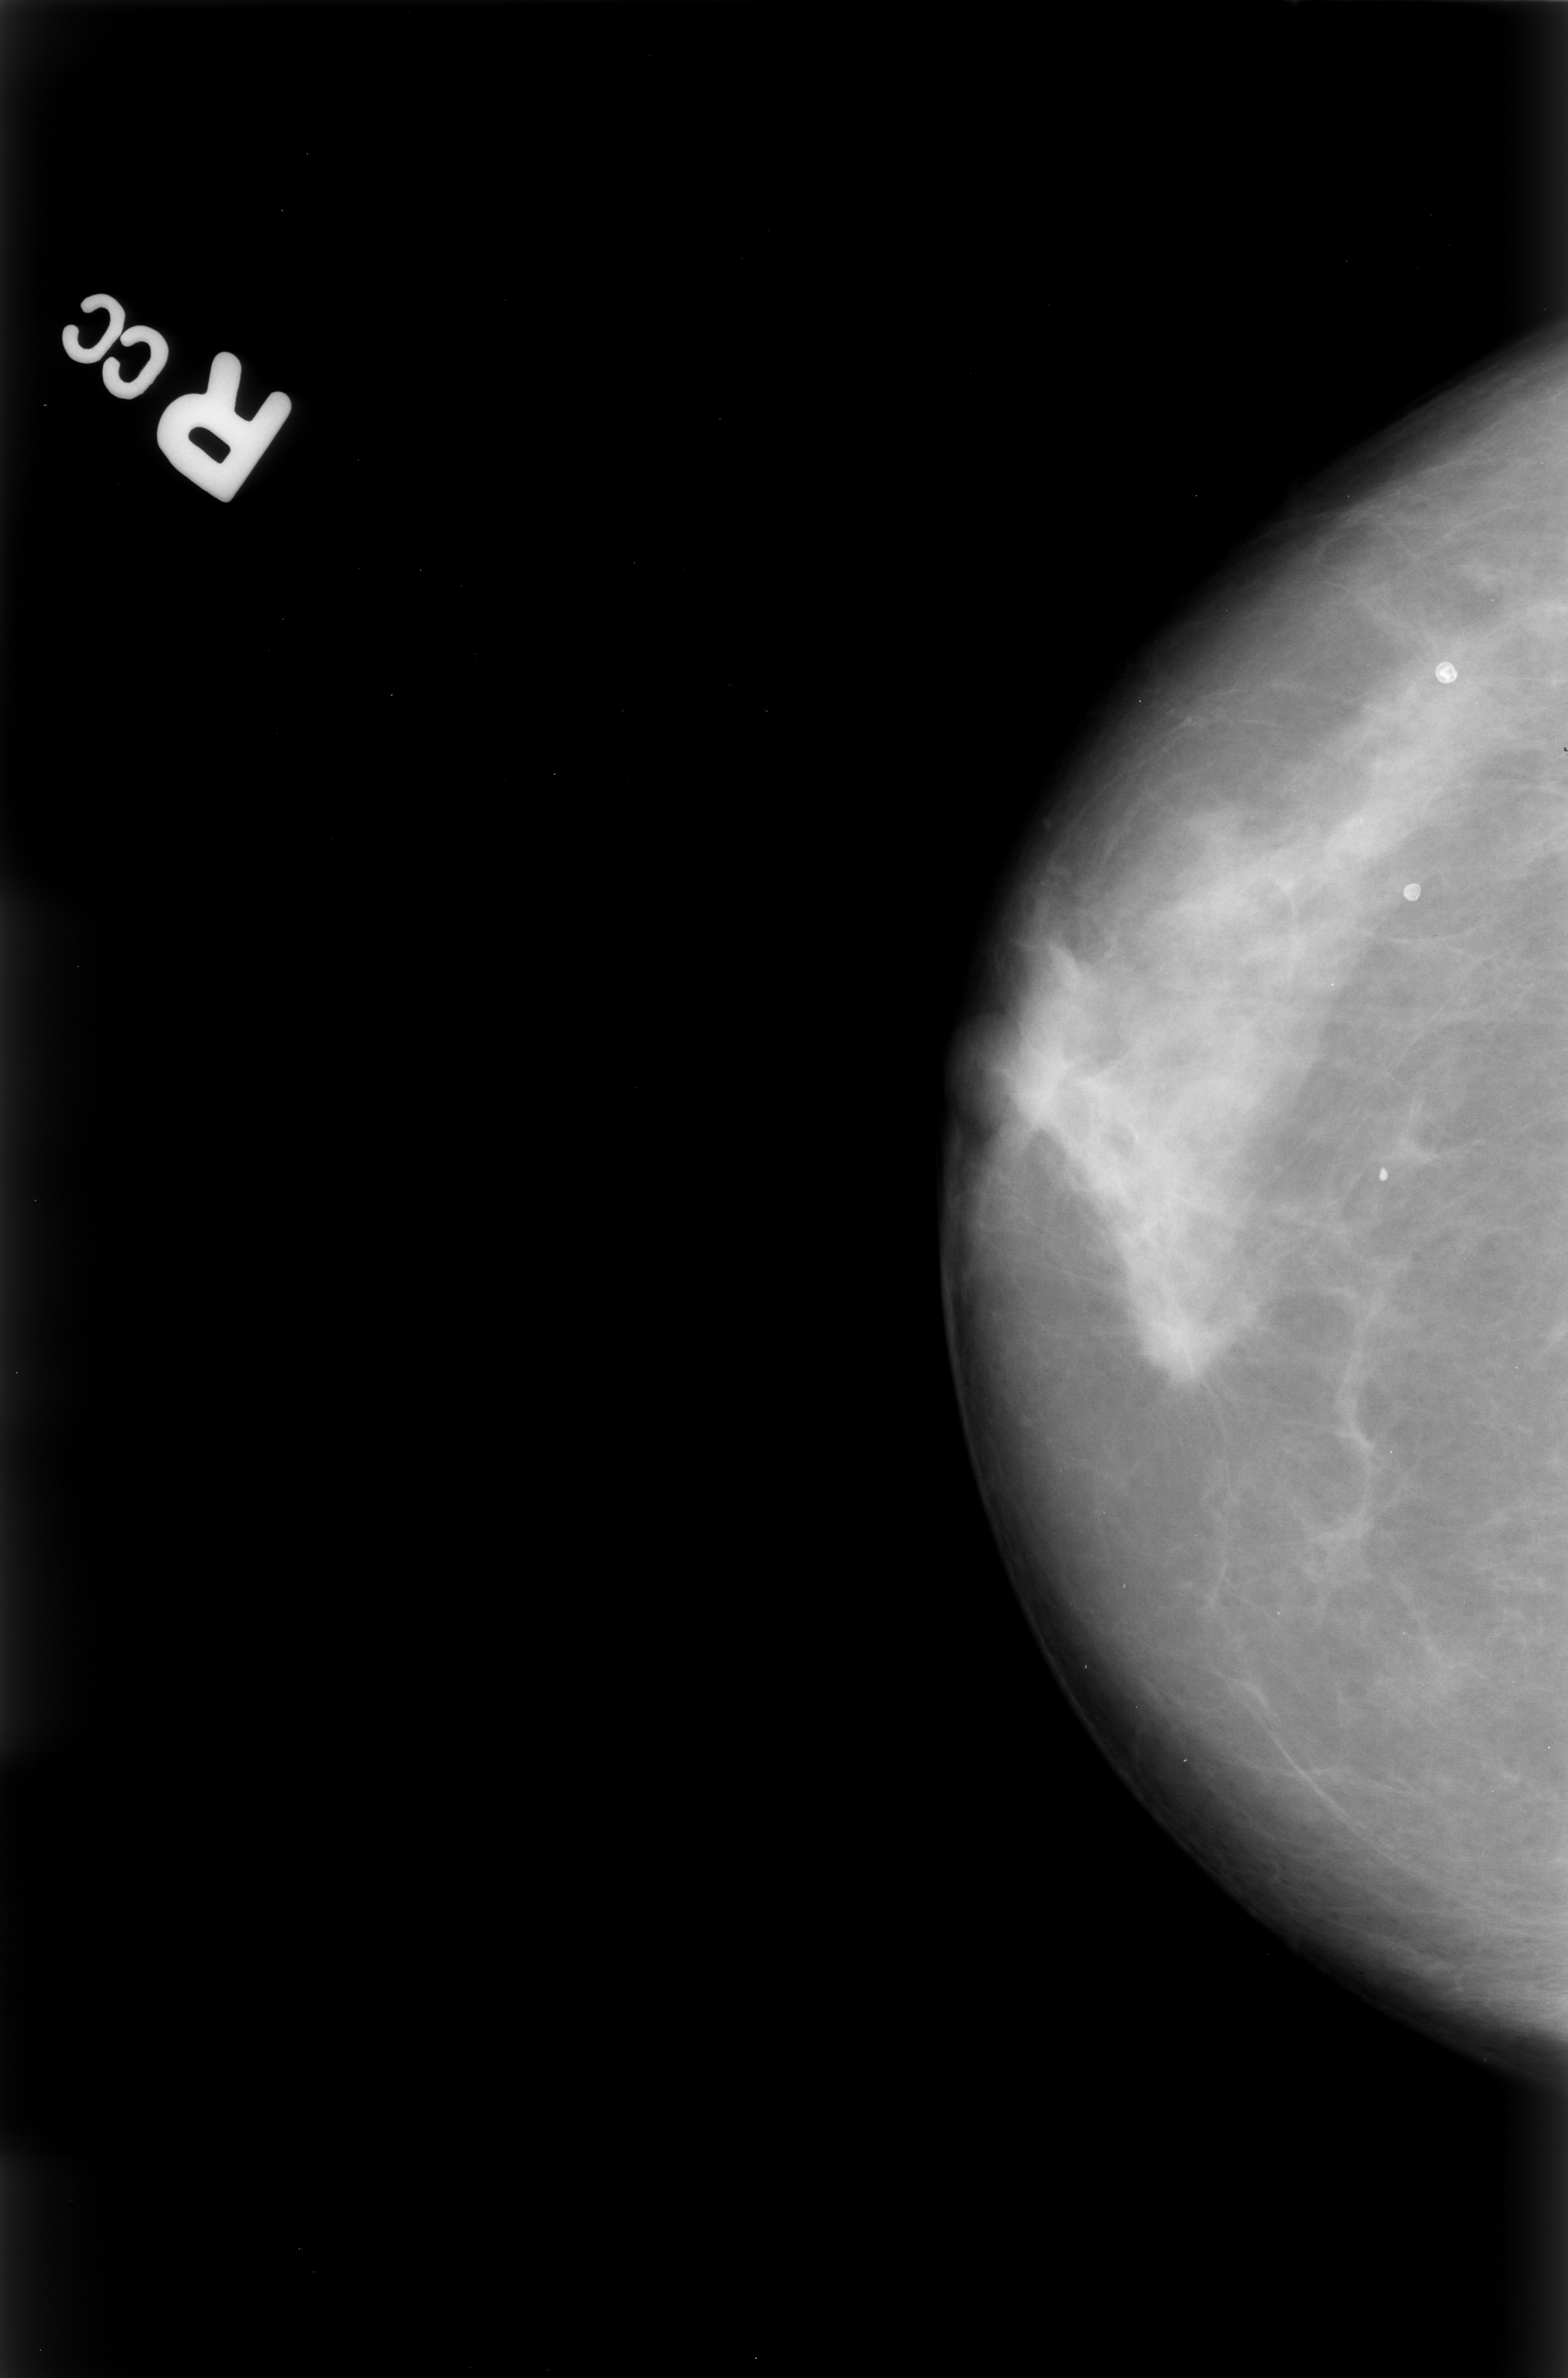
Digitized screen-film mammogram; right breast; CC view.
- Marked abnormality: mass, shape irregular / architectural distortion, margins spiculated; BI-RADS assessment category 5; subtlety rating 4 on a 1 (subtle) to 5 (obvious) scale; pathology (as recorded): malignant.